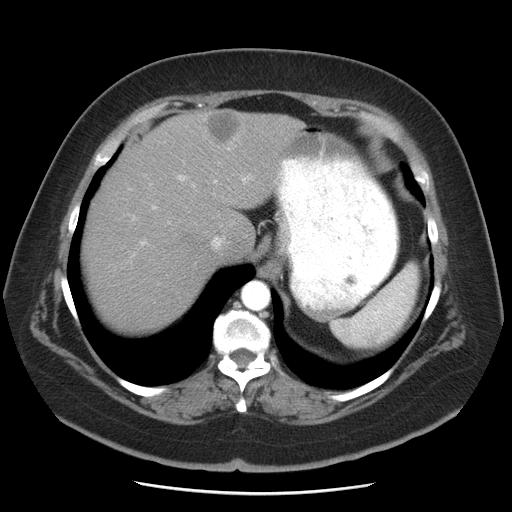
Contrast-enhanced abdominal CT, one axial slice; slice 38 of 55 in the series (ordered by position); 120 kVp; soft-tissue window (W 400 / L 40 HU); 5 mm slice thickness; 512 × 512 image matrix, field of view 380 × 380 mm. Female patient, age 52 years. From the clinical record (not read from this slice): diagnosis: colorectal cancer liver metastases, imaged before liver resection.
Structures marked on this image (outlined manually by an expert reader):
- hepatic veins: bounding box <212,237,224,249> (left, top, right, bottom; pixels)
- liver: <81,109,305,335>
- planned liver remnant (the part of the liver to remain after resection): <81,161,211,335>
- portal vein (with intrahepatic branches): <141,143,253,244>
- liver metastasis: <203,110,245,145>